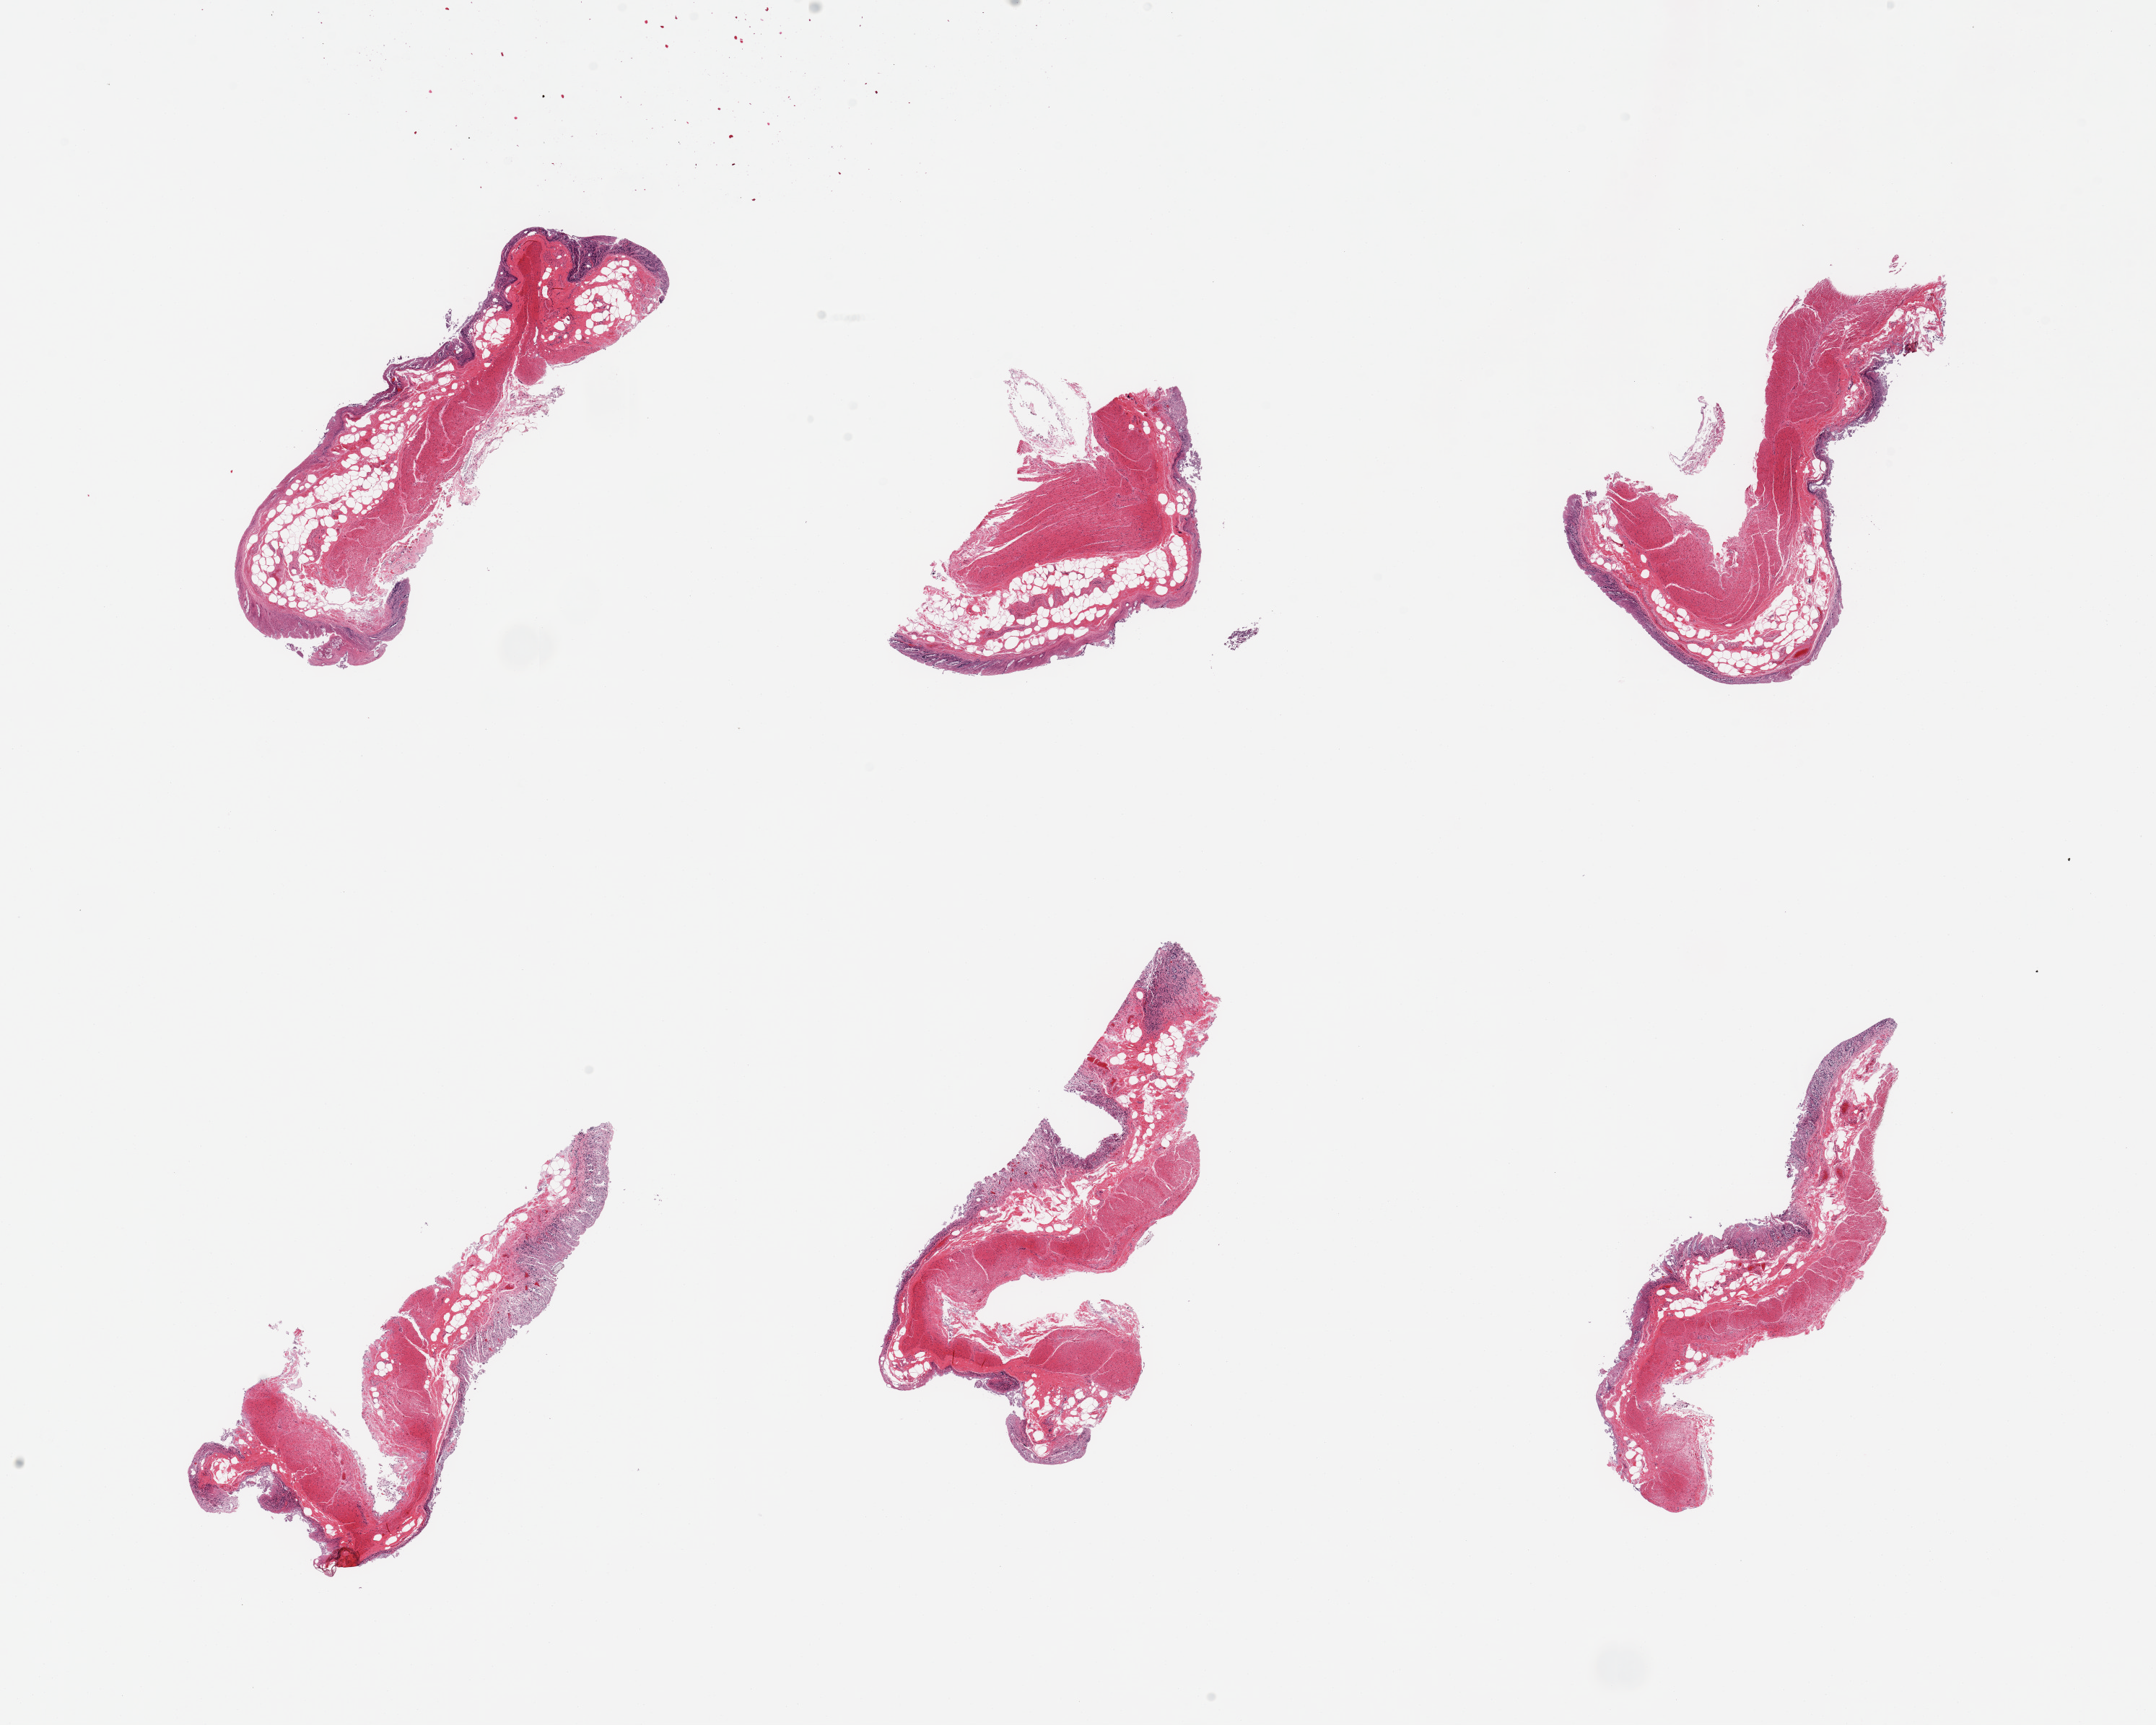
Haematoxylin and eosin whole-slide image — shown as a low-resolution overview of the whole scanned area (about 23.6 x 18.9 mm, from a 20x scan); PAXgene-fixed, paraffin-embedded tissue; sampled site (target tissue): transverse colon; tissue donor sample. Donor: male.
Review note (as recorded): 6 pieces; full thickness sections, mucosa autolyzed (3), muscularis (2).